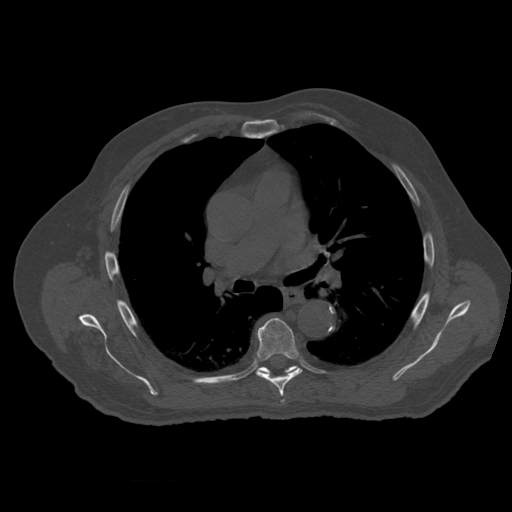
CT including the spine, one axial slice. Position 377 of 399 along the scan axis. Bone window (W 1800 / L 400 HU). 512 × 512 image matrix, field of view 407 × 407 mm. Patient age 73 years. Case-level facts recorded for this patient, not image findings: primary cancer: prostate; vertebrae with lytic lesions (as recorded): L2.
Outlined on this slice (semi-automatically segmented with operator editing):
- T6 vertebra: box from (x=257, y=318) to (x=303, y=397) px
- T7 vertebra: (x=259, y=366)–(x=298, y=374)